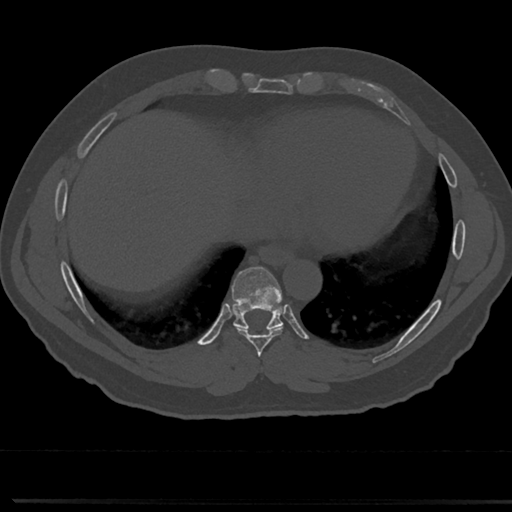
CT including the spine, one axial slice; position 332 of 817 along the scan axis; reconstruction kernel Br40s/3; 120 kVp; bone window (W 1800 / L 400 HU); 0.5 mm slice thickness; 512 × 512 image matrix. Male patient, age 61 years. Case-level facts recorded for this patient, not image findings: primary cancer: prostate.
Structures marked on this image (semi-automatic segmentation, software-assisted and operator-edited):
- T7 vertebra: box from (x=259, y=349) to (x=266, y=377) px
- T8 vertebra: (x=211, y=270)–(x=310, y=356)